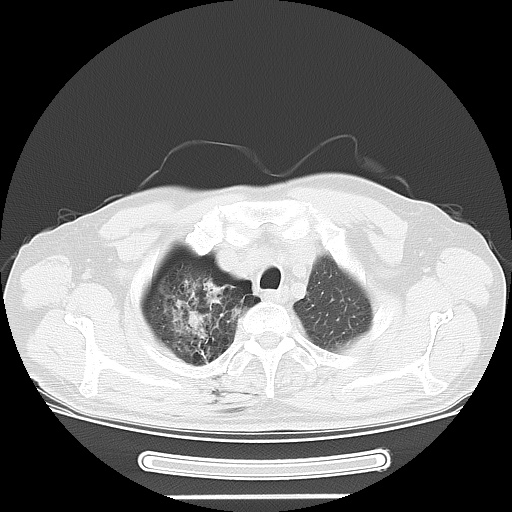
Chest CT, one axial slice; position 50 of 57 along the scan axis; reconstruction kernel LUNG; 120 kVp; lung window (W 1500 / L -600 HU); 5 mm slice thickness; 512 × 512 image matrix. Patient: male, 61 years. Case-level facts recorded for this patient, not image findings: clinical TNM (as recorded): T1c N3 M1b.
Structures marked on this image (rectangle marked by the reading radiologist):
- lung tumour (recorded histology: adenocarcinoma): bounding box <155,270,253,365> (left, top, right, bottom; pixels)